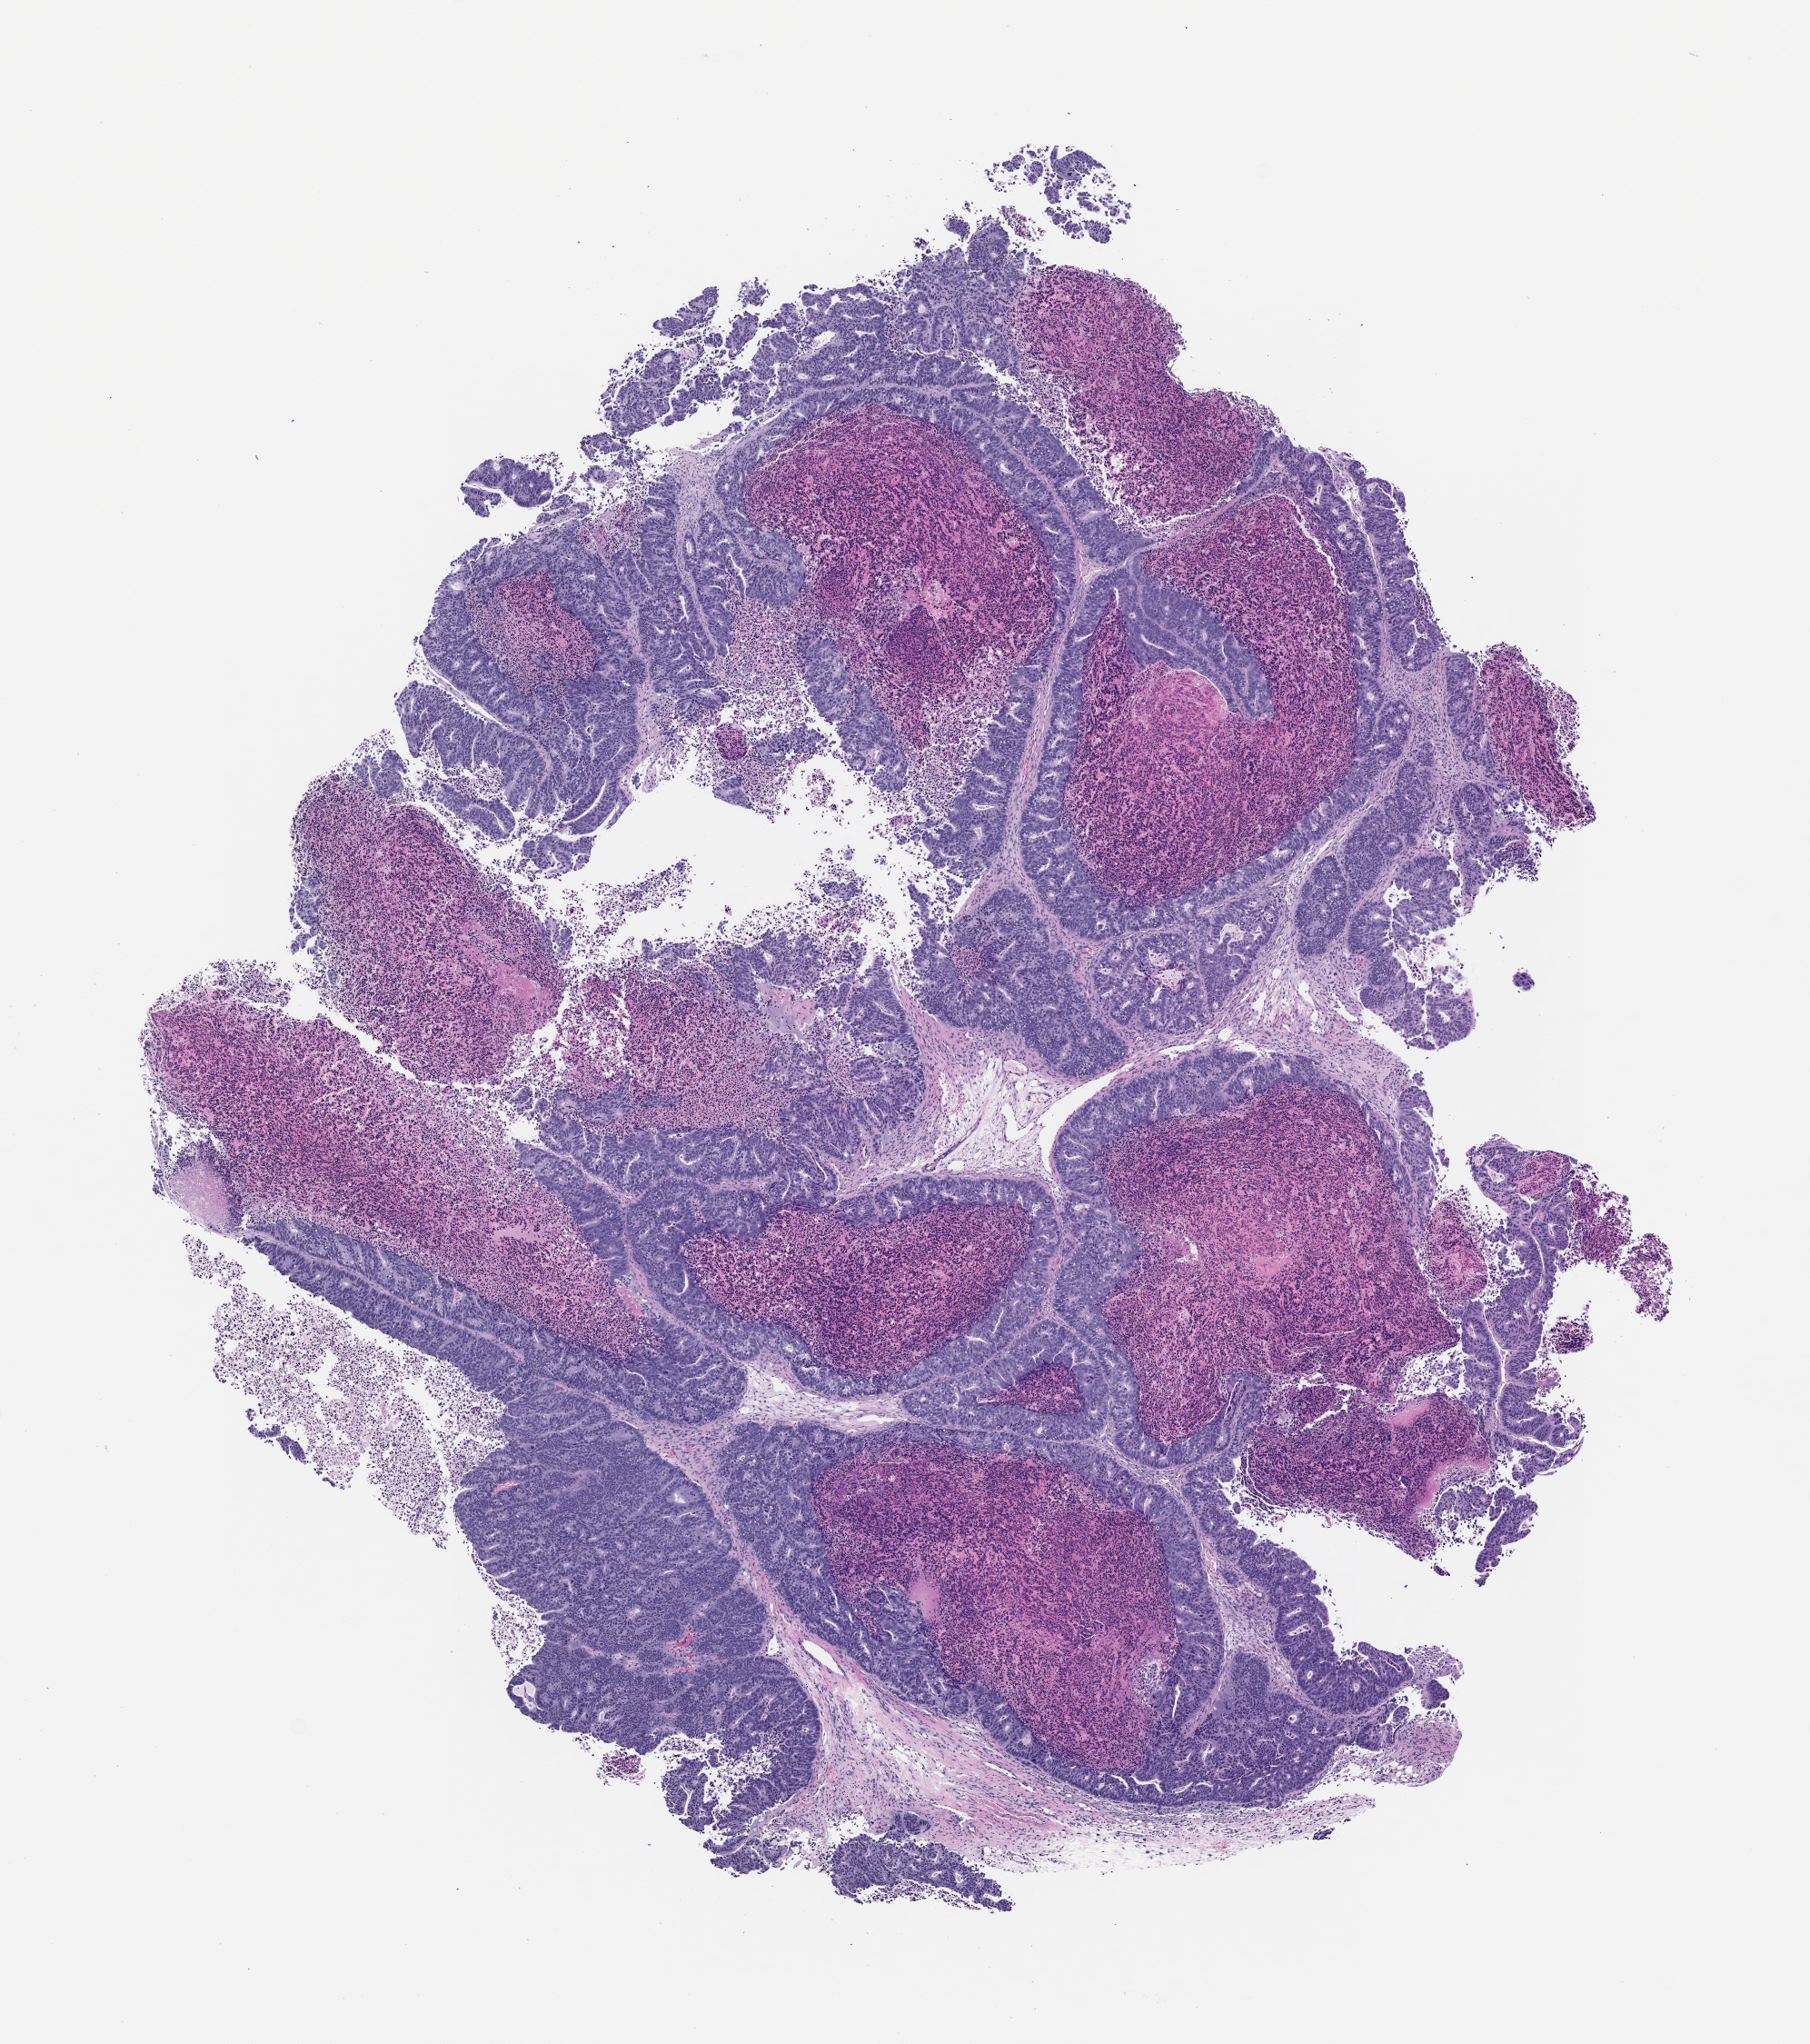
Whole-slide image, haematoxylin and eosin: patient-derived xenograft (human tumor grown in a mouse), passage 2, a low-resolution overview of the entire scanned area, about 8.0 x 9.0 mm, FFPE section, originating tumor site category: colon.
Originating patient diagnosis: Colon Adenocarcinoma.